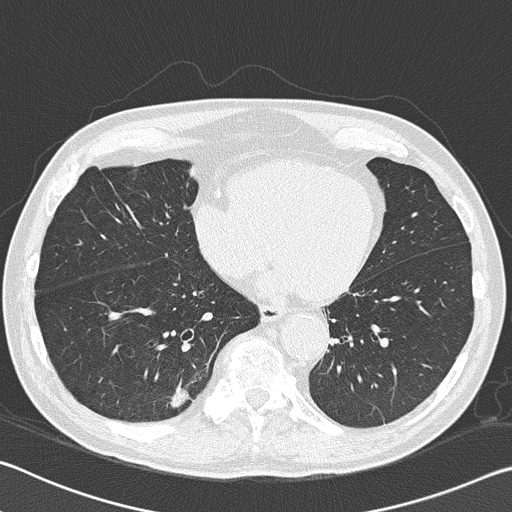
Axial slice from a low-dose chest CT screening exam. Baseline annual screen. Lung window (W 1500 / L -600 HU). 2 mm slice thickness. Male participant, aged 74 years at enrolment. Current smoker at enrolment.
Expert reader's lesion annotation, bounding box (x1, y1, x2, y2) in pixels: (148, 369, 213, 429). Screening reader's record for this exam (one nodule recorded; not confirmed to be the boxed lesion): non-calcified nodule or mass ≥4 mm, right lower lobe, 13 × 11 mm, spiculated (stellate) margins, soft tissue attenuation. Official screen result: positive, change unspecified: nodule(s) >= 4 mm or enlarging nodule(s), mass(es), or other non-specific abnormalities suspicious for lung cancer. Later outcome: lung cancer diagnosed 414 days after this screen — bronchiolo-alveolar adenocarcinoma, NOS, right lower lobe, moderately differentiated (G2), stage IA (AJCC 6th edition), 16 mm at pathology.